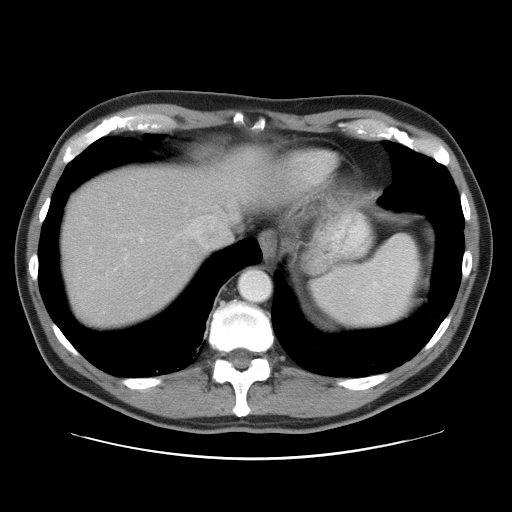
Contrast-enhanced abdominal CT, one axial slice; position 46 of 52 along the scan axis; reconstruction kernel STANDARD; 120 kVp; intravenous contrast given; soft-tissue window (W 400 / L 40 HU); 512 × 512 image matrix, field of view 393 × 393 mm. Male patient, age 70 years. From the clinical record (not read from this slice): diagnosis: colorectal cancer liver metastases, imaged before liver resection; multiple liver metastases: yes.
Annotated regions visible in this slice (manually delineated by an expert):
- hepatic veins: bounding box (x1, y1, x2, y2) in pixels: (177, 199, 219, 243)
- liver: (60, 148, 264, 330)
- planned liver remnant (the part of the liver to remain after resection): (147, 148, 266, 213)